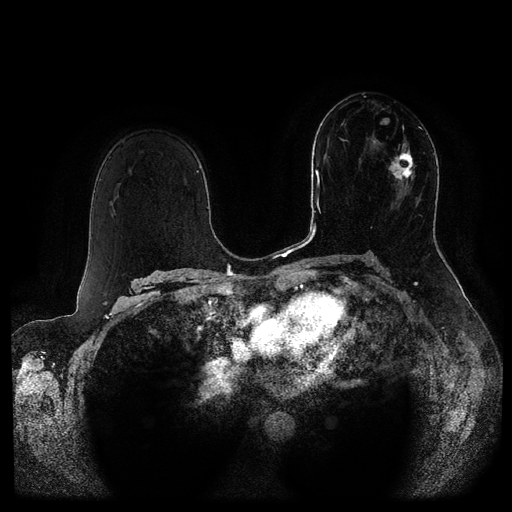
Breast MRI (dynamic contrast-enhanced, multi-phase), one axial slice; slice 57 of 116 in the series (ordered by position); dynamic contrast-enhanced series, time point 2 of 5 at this slice position (early post-contrast); 1.5 T; TE 2.6 ms, TR 5.3 ms; 512 × 512 image matrix, field of view 370 × 370 mm. Patient: female, 51 years.
Structures marked on this image (semi-automatically segmented with operator editing):
- breast lesion (labelled 'tumour' in the annotation; benign lesions carry a separate 'benign' label): bounding box (x1, y1, x2, y2) in pixels: (373, 125, 416, 186)